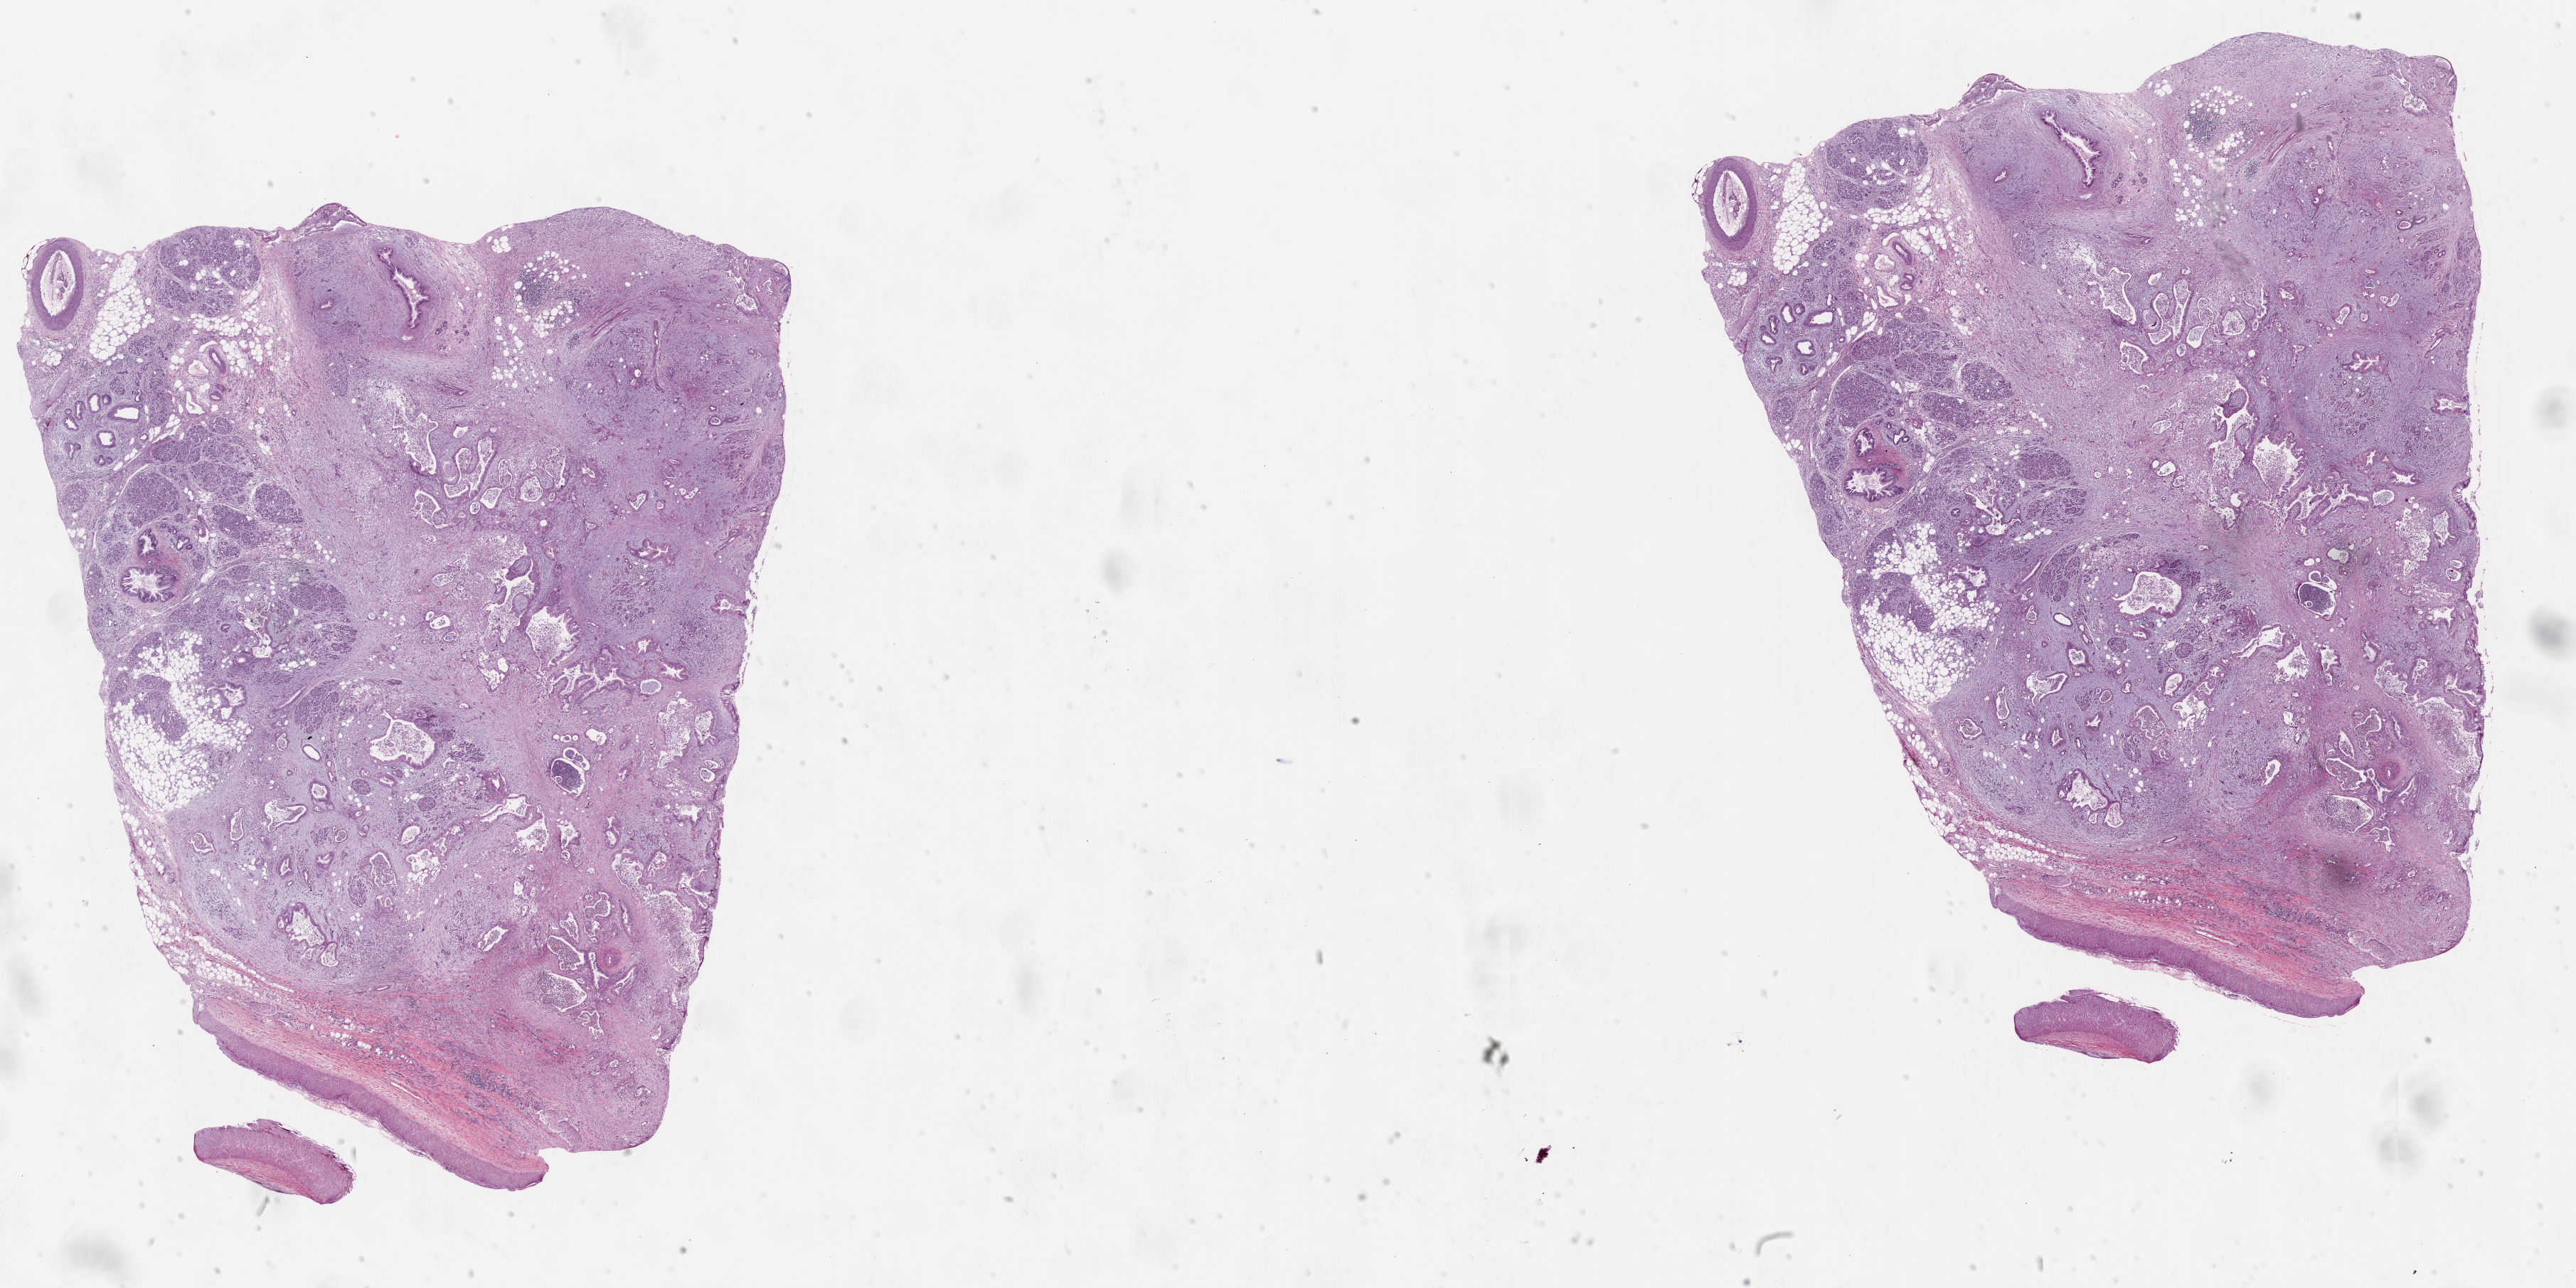
H&E-stained whole-slide image — whole scanned area (about 29.0 x 14.5 mm, from a 20x scan) shown as a low-resolution overview; FFPE section; pancreas, primary tumour sample. Patient: female, age at initial diagnosis 48 years. Histologic grade: G2 (moderately differentiated).
Lymph nodes positive (case pathology): 0 of 1 examined. AJCC pathologic stage: IIA. Histologic diagnosis: Infiltrating duct carcinoma, NOS (head of pancreas).